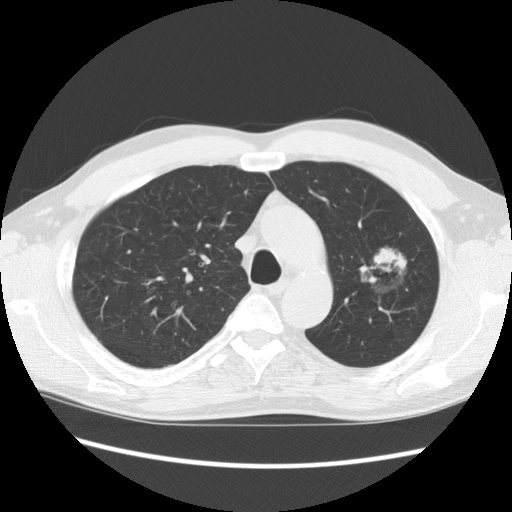
Chest CT (low-dose screening protocol), one axial image. Second screening round (one year after baseline). Lung window (W 1500 / L -600 HU). 2.5 mm slice thickness. Slice 101 of 139 in the series. Male, age 61 years at enrolment.
Lesion marked by an expert reader, bounding box (x1, y1, x2, y2) in pixels: (347, 225, 424, 300). Screening reader's record for this exam (one nodule recorded; not confirmed to be the boxed lesion): non-calcified nodule or mass ≥4 mm, left upper lobe, 34 × 32 mm, poorly defined margins, mixed attenuation, pre-existing on the prior screen: yes; interval growth: no. Official screen result: positive, no significant change: stable abnormalities potentially related to lung cancer, unchanged since the prior screening exam.